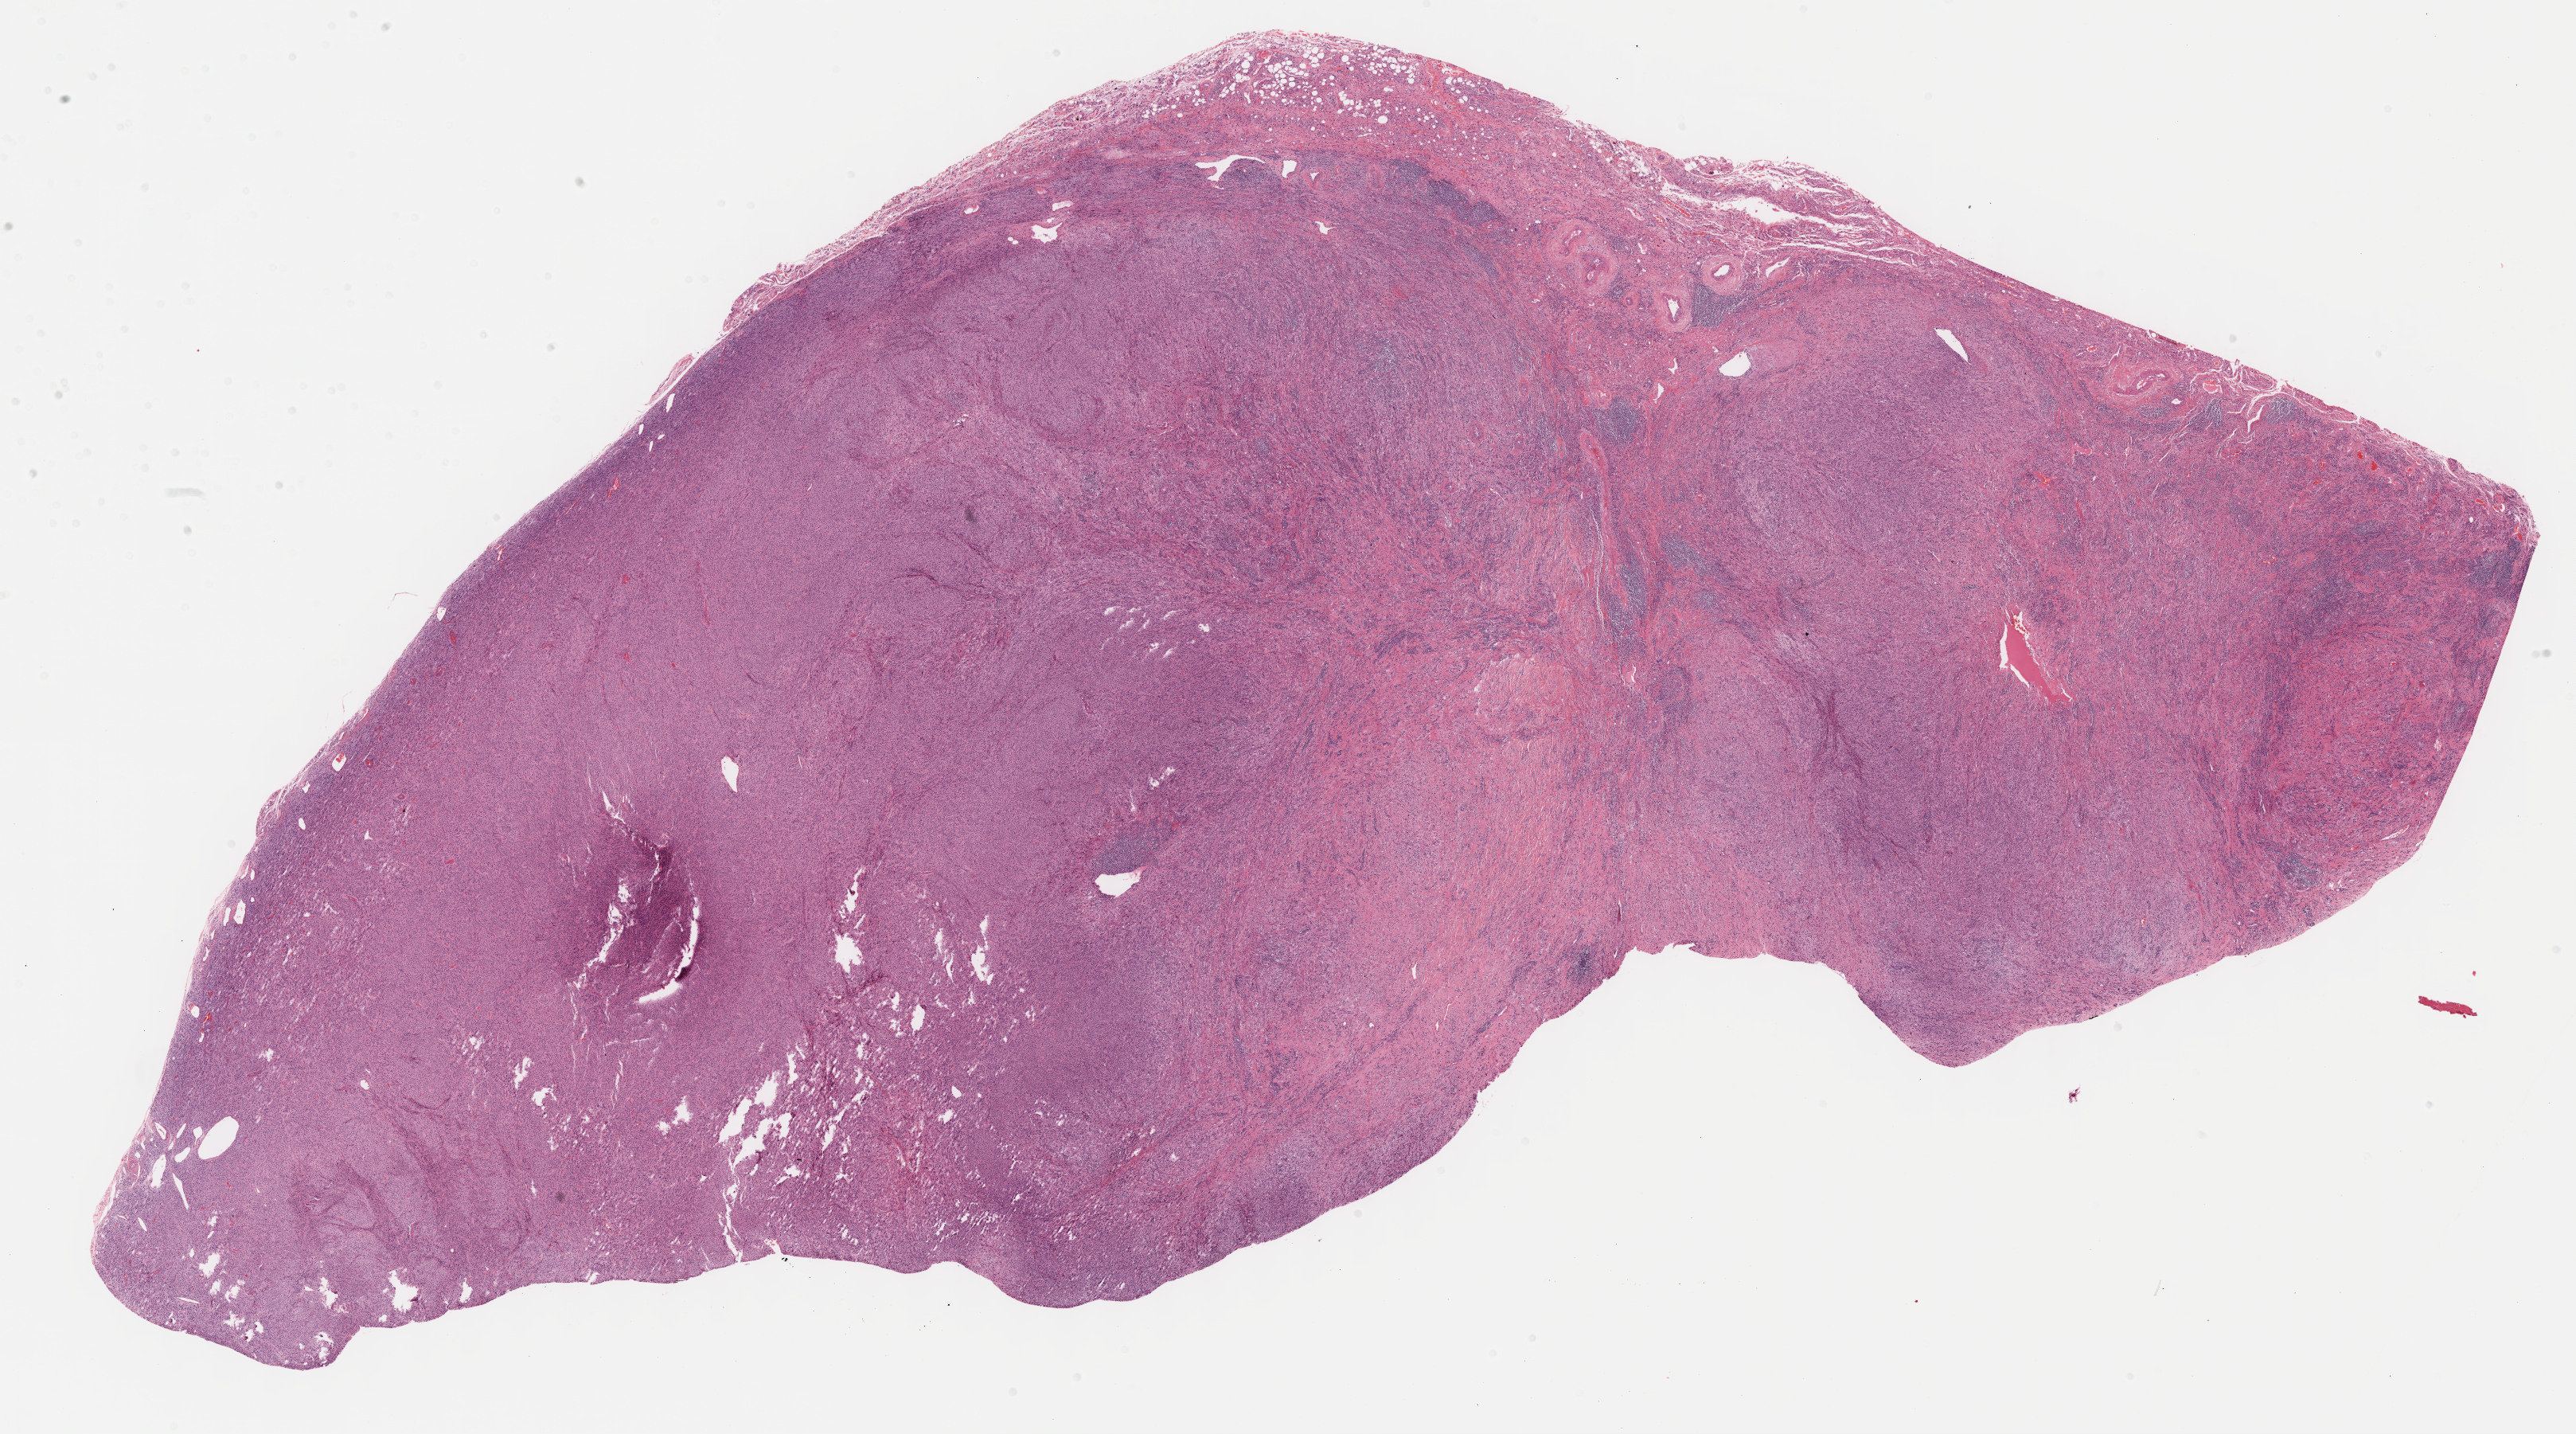
Digitized H&E-stained tissue section (whole slide) — shown as a low-resolution overview of the whole scanned area (about 26.2 x 14.6 mm, from a 40x scan). Formalin-fixed paraffin-embedded (FFPE) diagnostic section. Primary tumour sample from the connective, subcutaneous and other soft tissues. Female patient; age at initial diagnosis 73 years.
Pathologic diagnosis: Dedifferentiated liposarcoma (connective, subcutaneous and other soft tissues of lower limb and hip).